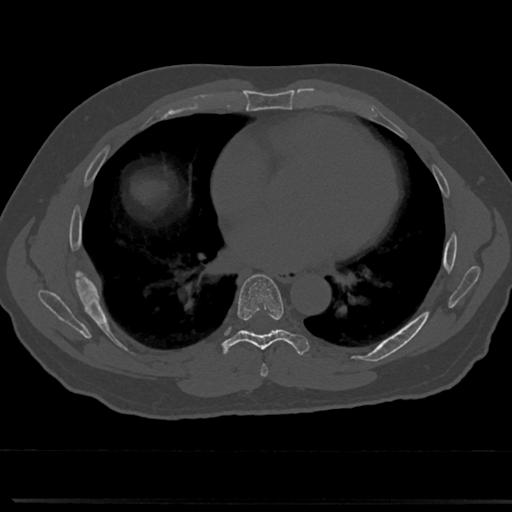
CT including the spine, one axial slice. Slice 406 of 817 in the series (ordered by position). Reconstruction kernel Br40s/3. 120 kVp. Bone window (W 1800 / L 400 HU). 0.5 mm slice thickness. 512 × 512 image matrix, field of view 355 × 355 mm. Male patient, age 61 years. From the clinical record (not read from this slice): primary cancer: prostate.
Outlined on this slice (semi-automatic segmentation, software-assisted and operator-edited):
- T6 vertebra: bounding box [x1, y1, x2, y2] px = [260, 340, 319, 371]
- T7 vertebra: [215, 275, 308, 358]